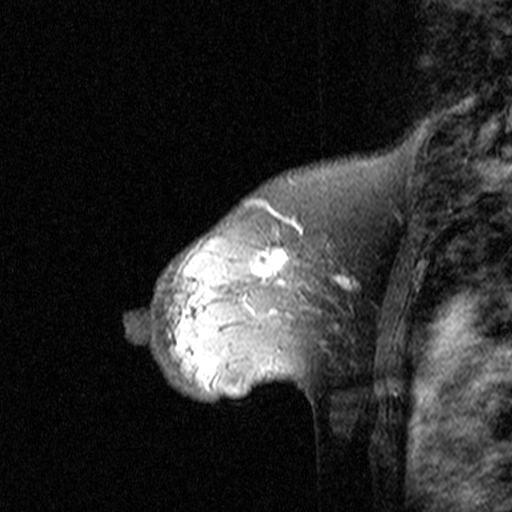
Breast MRI (dynamic contrast-enhanced), one sagittal slice. Slice 31 of 44 in the series (ordered by position). Dynamic contrast-enhanced study with each time point stored as its own series, time point 2 of 3 at this slice position (early post-contrast, ordered by acquisition time). 1.5 T. TE 4.5 ms, TR 11 ms. 3 mm slice thickness. 512 × 512 image matrix, field of view 200 × 200 mm. Female patient, age 46 years. From the clinical record (not read from this slice): setting: breast cancer imaged before/during neoadjuvant chemotherapy; receptor status: HER2-positive.
Annotated regions visible in this slice (semi-automatic segmentation, software-assisted and operator-edited):
- analysis volume of interest (the breast-tissue region the enhancement analysis was run in; not a lesion): bounding box (x1, y1, x2, y2) in pixels: (144, 172, 359, 393)
- tumour enhancement mask (voxels above the 90 % enhancement threshold inside the analysis volume of interest): (160, 205, 353, 356)